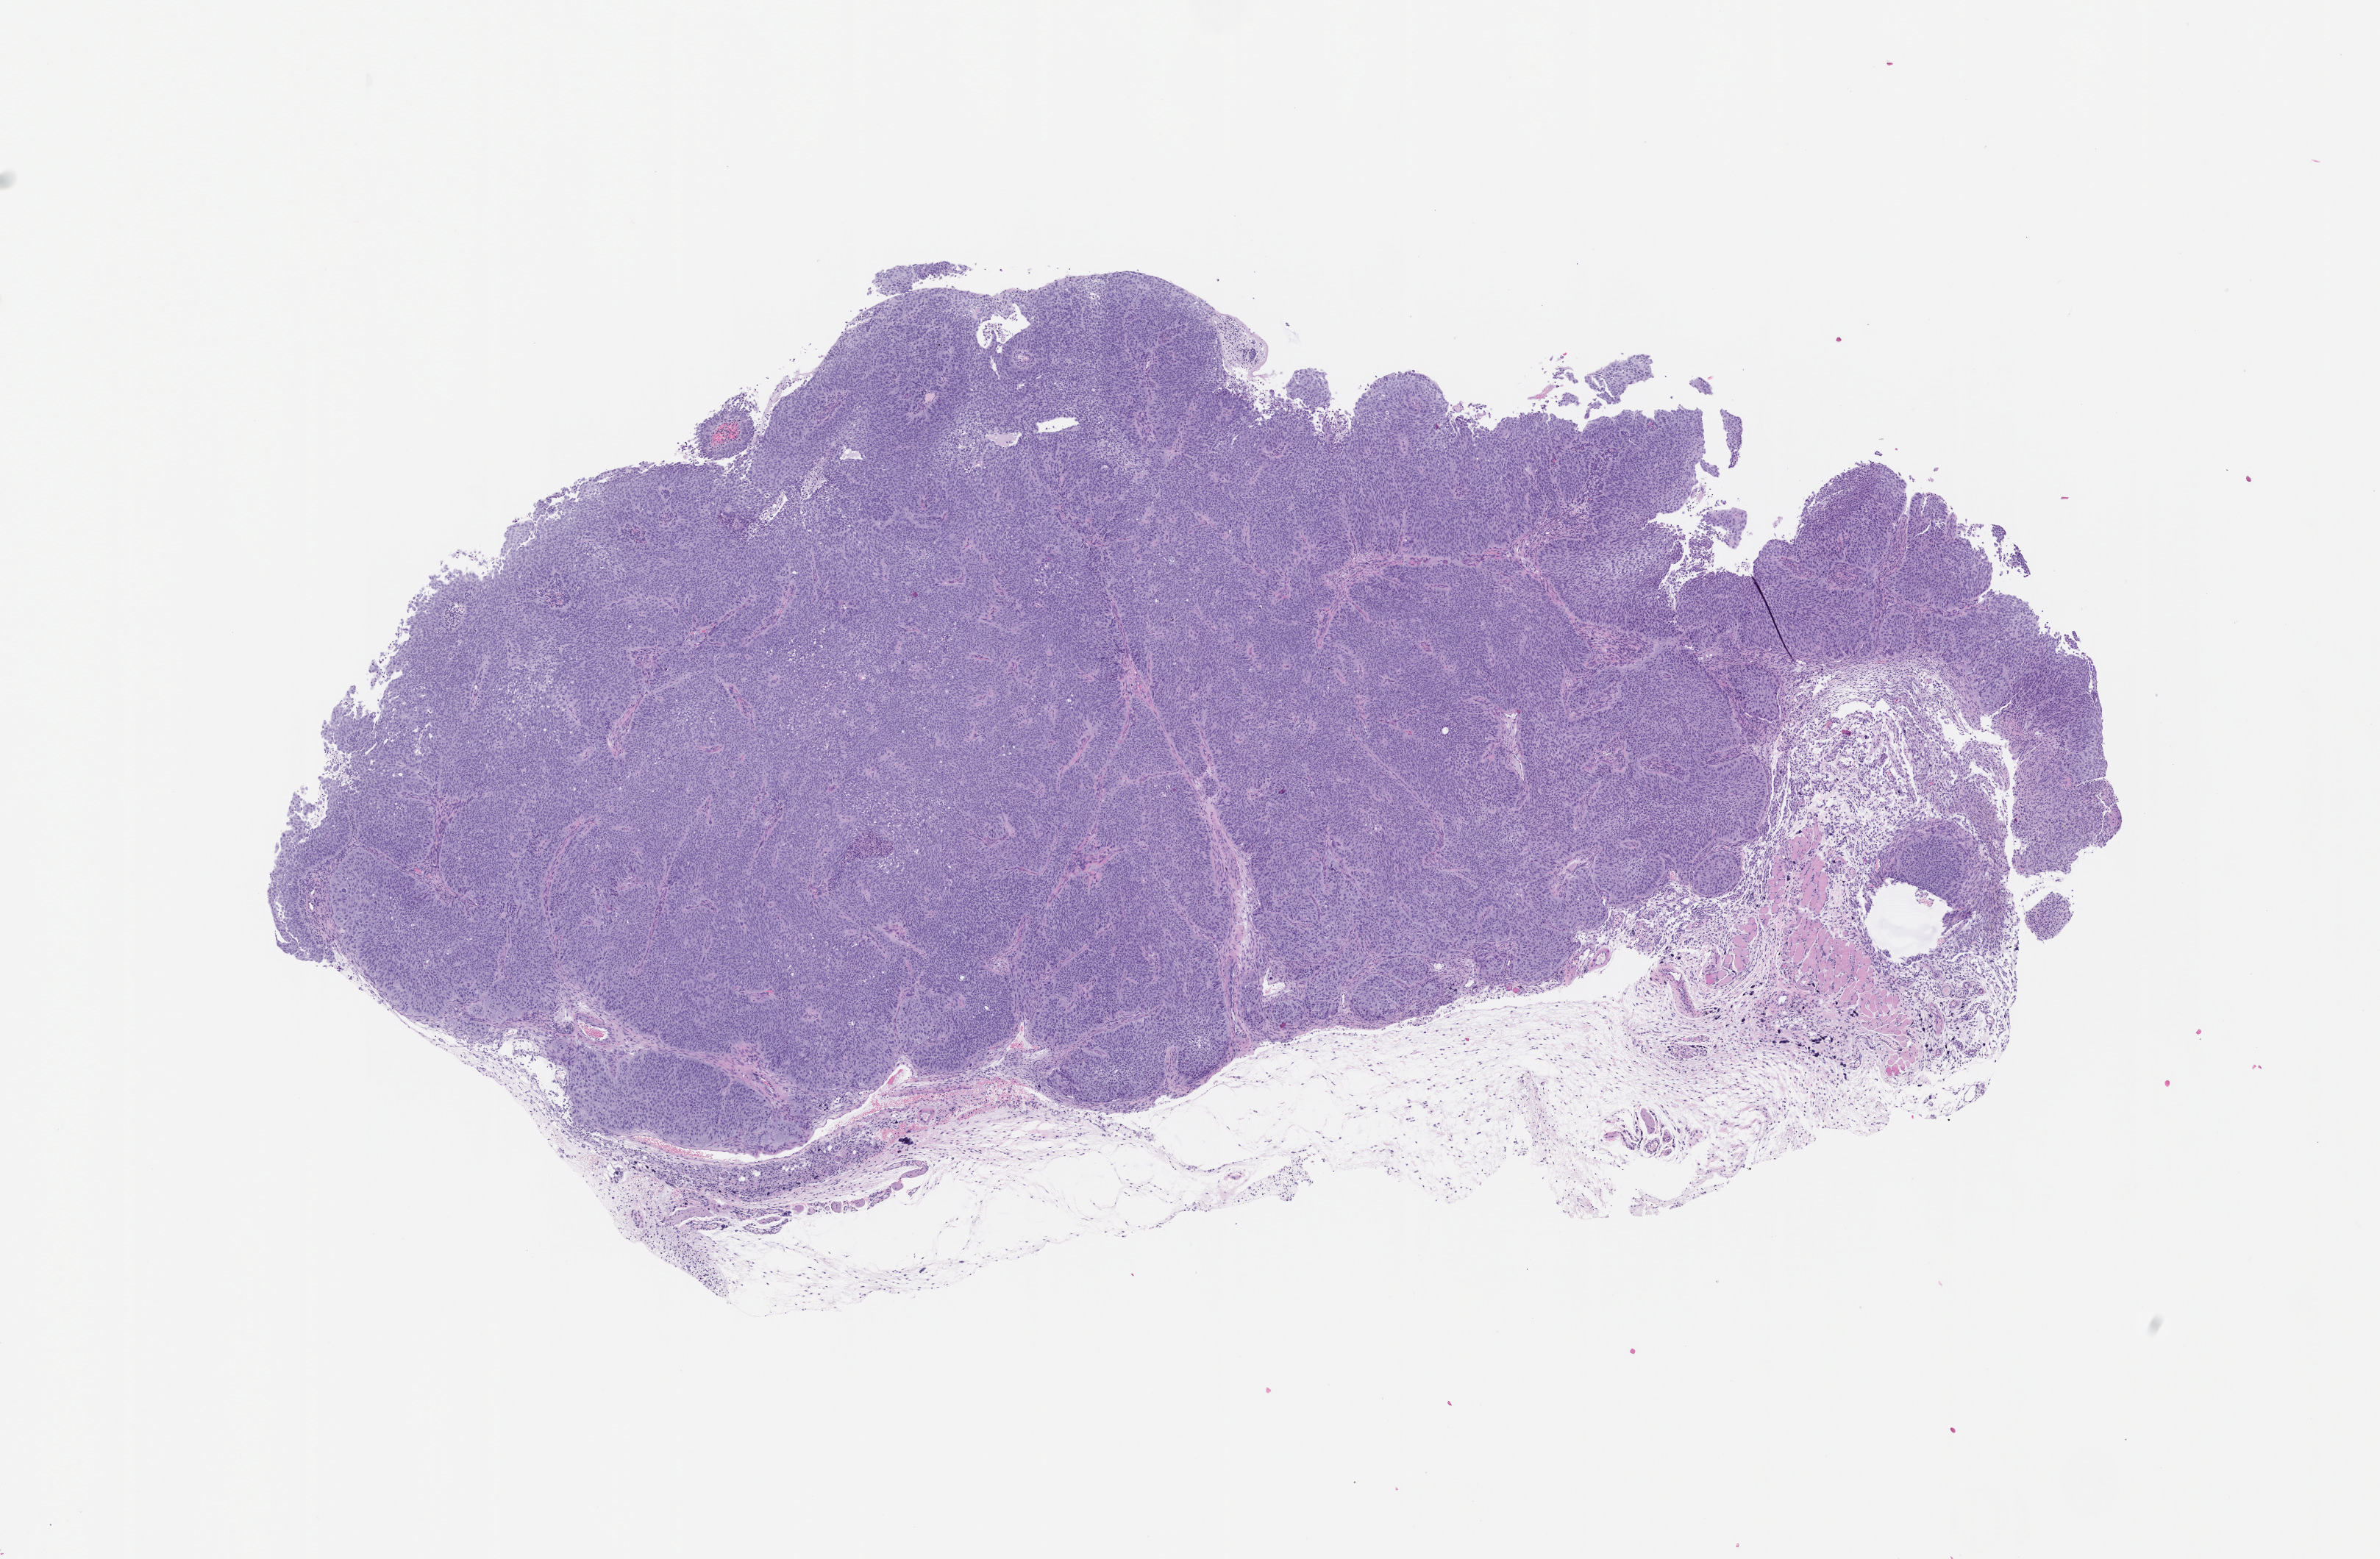
Haematoxylin and eosin whole-slide image of a patient-derived xenograft (PDX) tumor grown in a mouse, passage 0 — shown as a low-resolution overview of the whole scanned area (about 13.0 x 8.5 mm). FFPE section. Originating tumor site category: lung.
Originating patient diagnosis: Lung Squamous Cell Carcinoma.